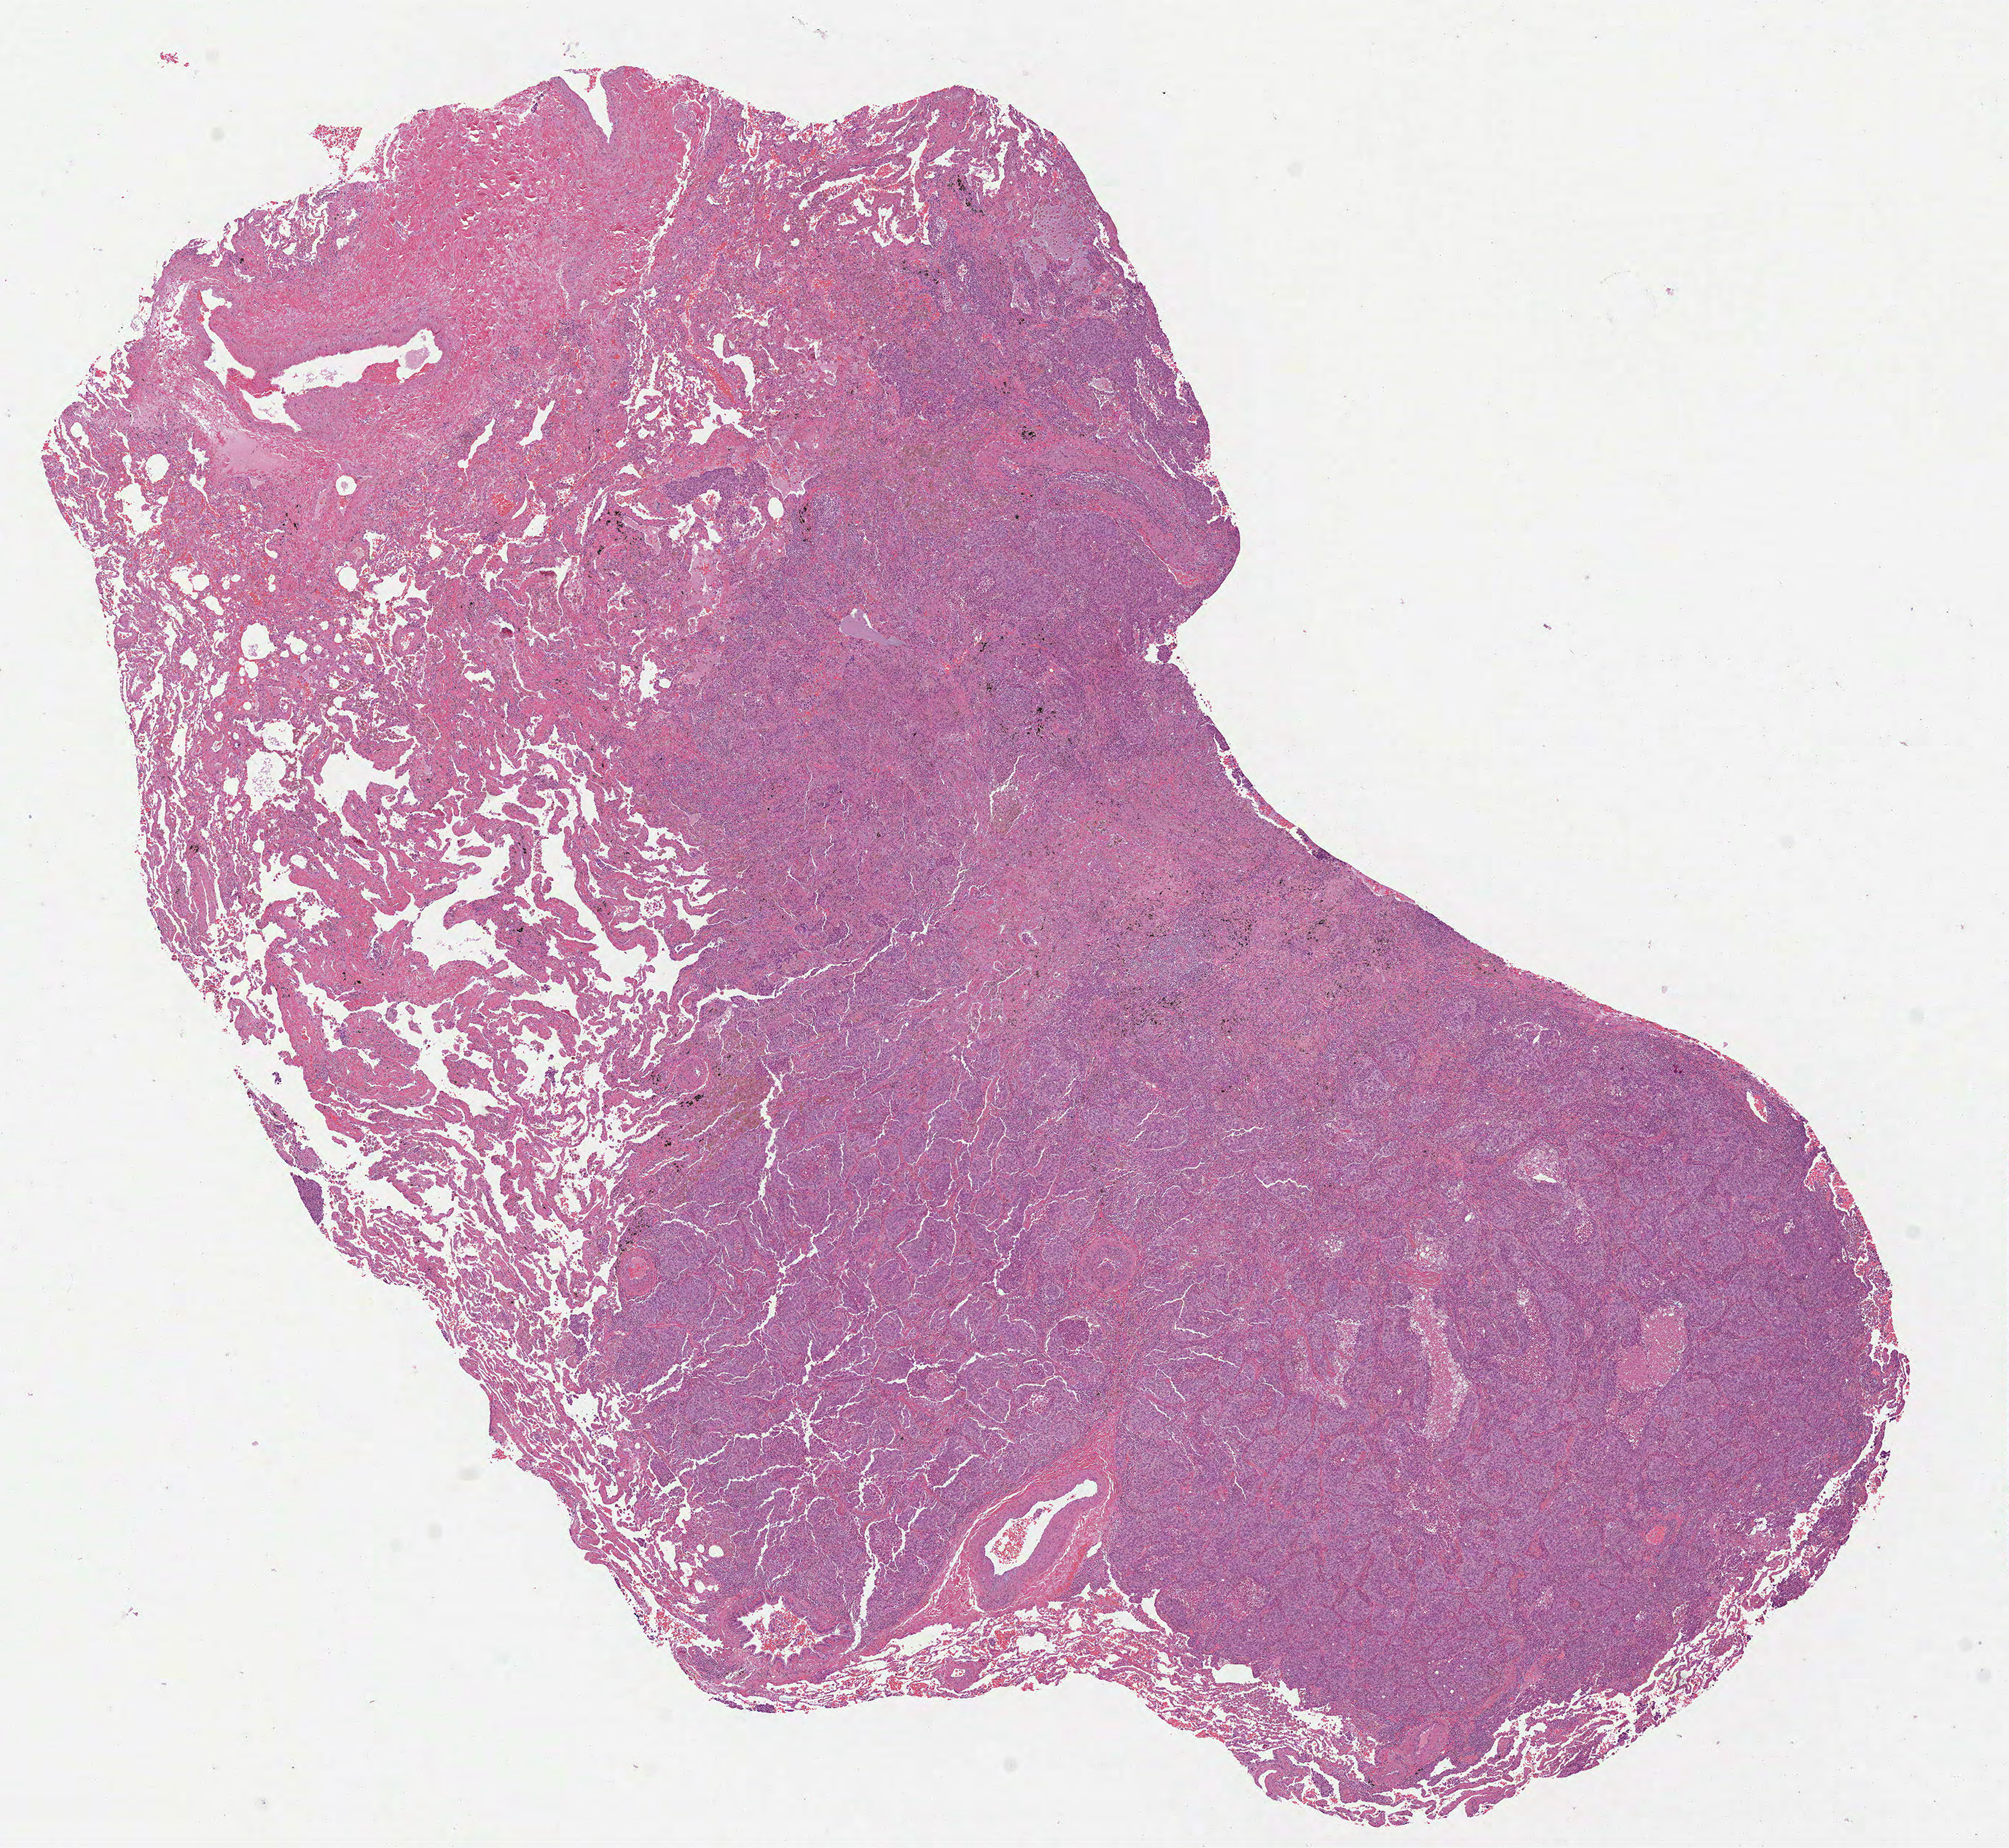
Whole-slide histology image, H&E, a low-resolution overview of the entire scanned area, about 11.1 x 10.2 mm, formalin-fixed paraffin-embedded (FFPE) diagnostic section, sample: primary tumour, lung. Male, age 60 years at initial diagnosis.
TNM: T1a N1 M1b. Laterality: left. AJCC pathologic stage: IV (7th edition). Pathologic diagnosis: Adenocarcinoma, NOS (upper lobe, lung).